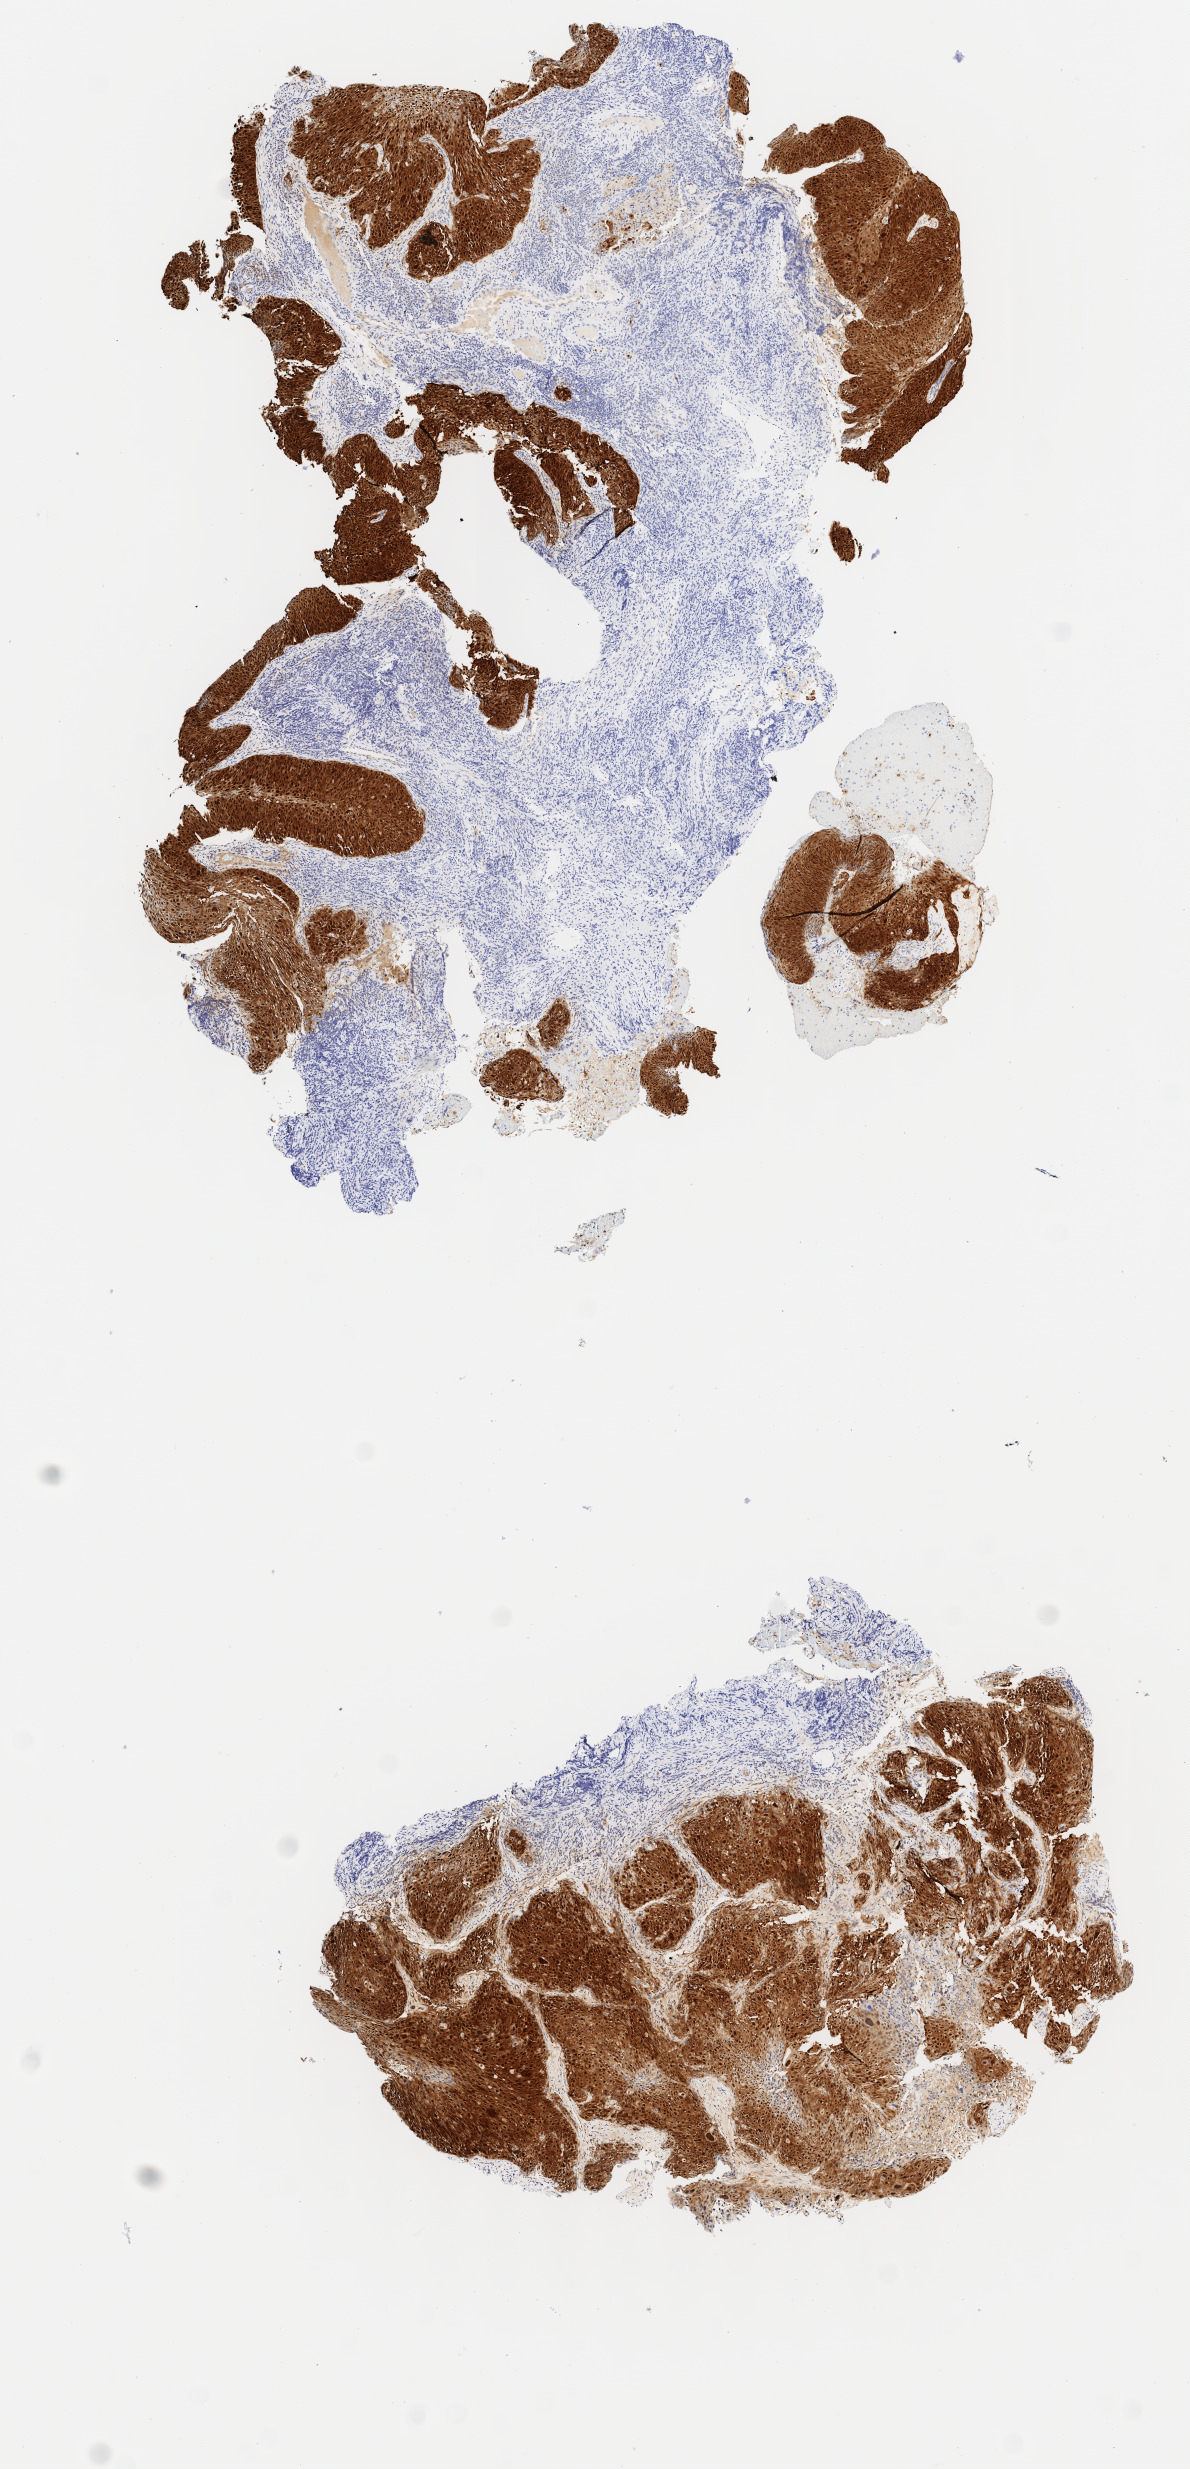
Whole-slide image, immunohistochemical stain for p16 (p16INK4a) — a low-resolution overview of the entire scanned area, about 4.7 x 9.8 mm, specimen: tumor tissue, anatomic site: cervix. Patient female; age 51 years.
• histologic diagnosis: Squamous cell carcinoma, large cell, nonkeratinizing, NOS